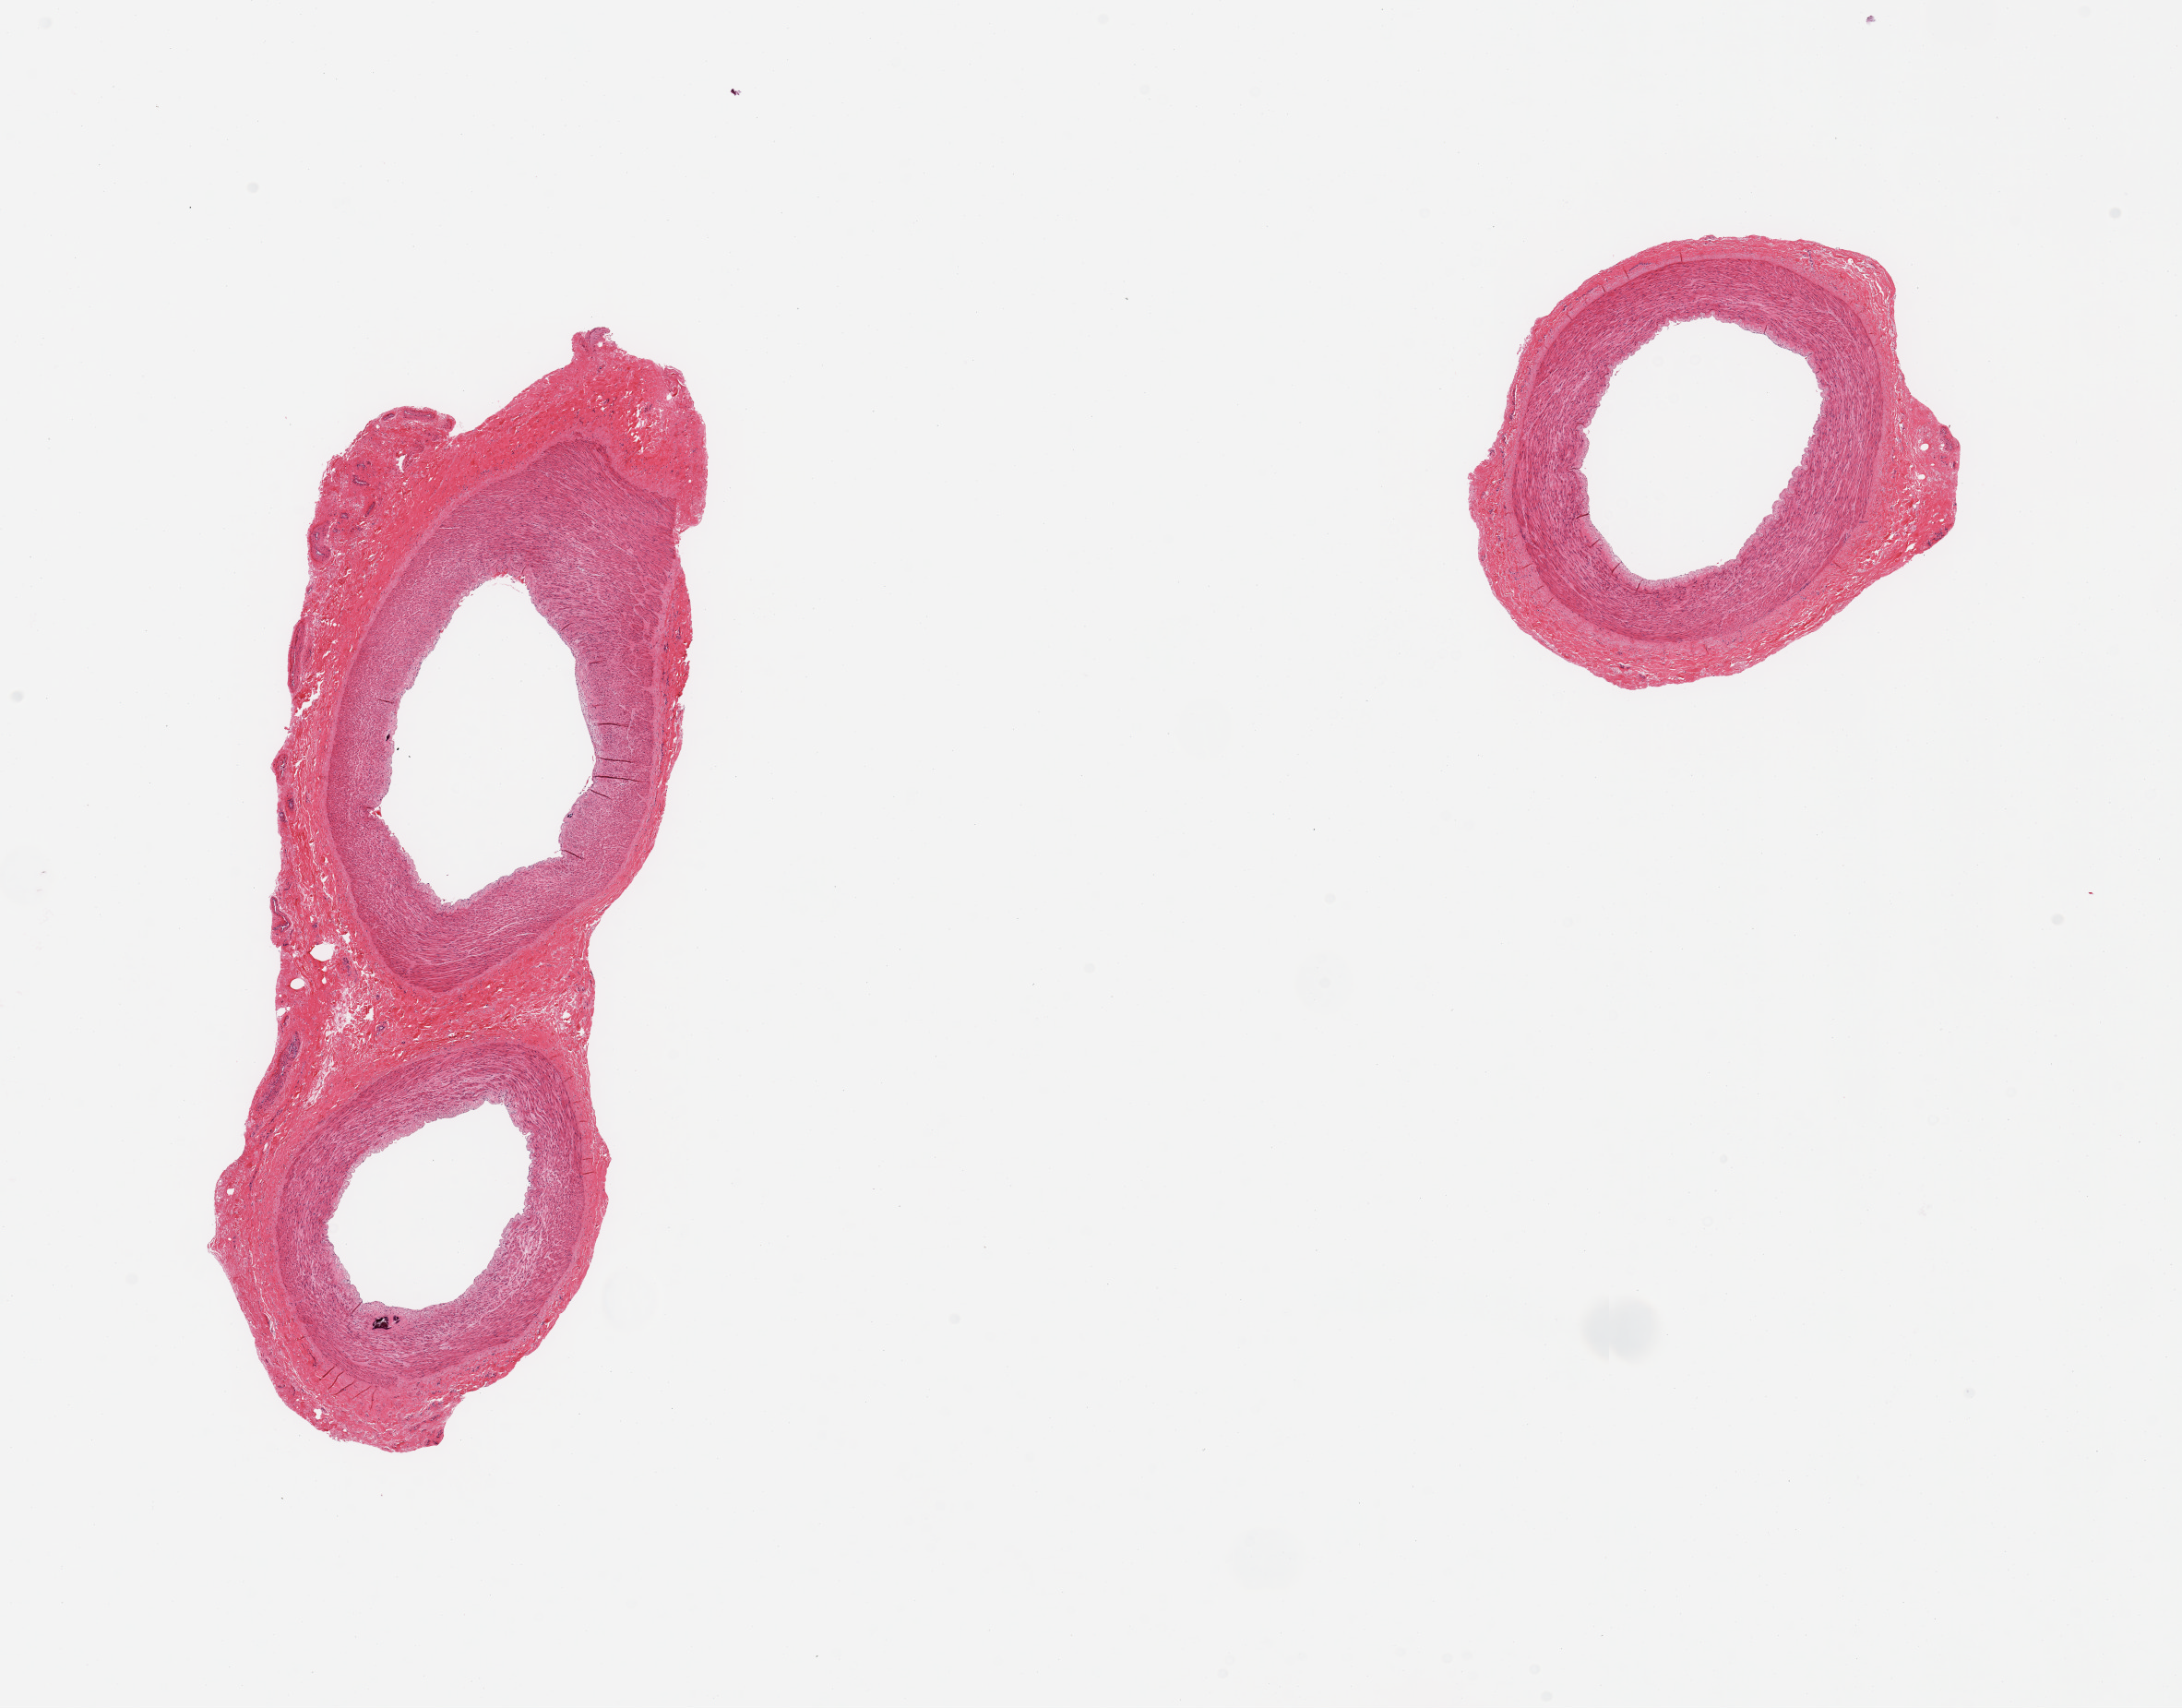
Digitized hematoxylin and eosin (H&E)-stained section — a low-resolution overview of the entire scanned area, about 18.7 x 14.6 mm. PAXgene-fixed, paraffin-embedded tissue. Sampled site (target tissue): tibial artery. Donor tissue sample. Male donor.
Pathologist's review note for this sample: 2 pieces, rim of adherent fascia up to ~1mm; no atherosis.